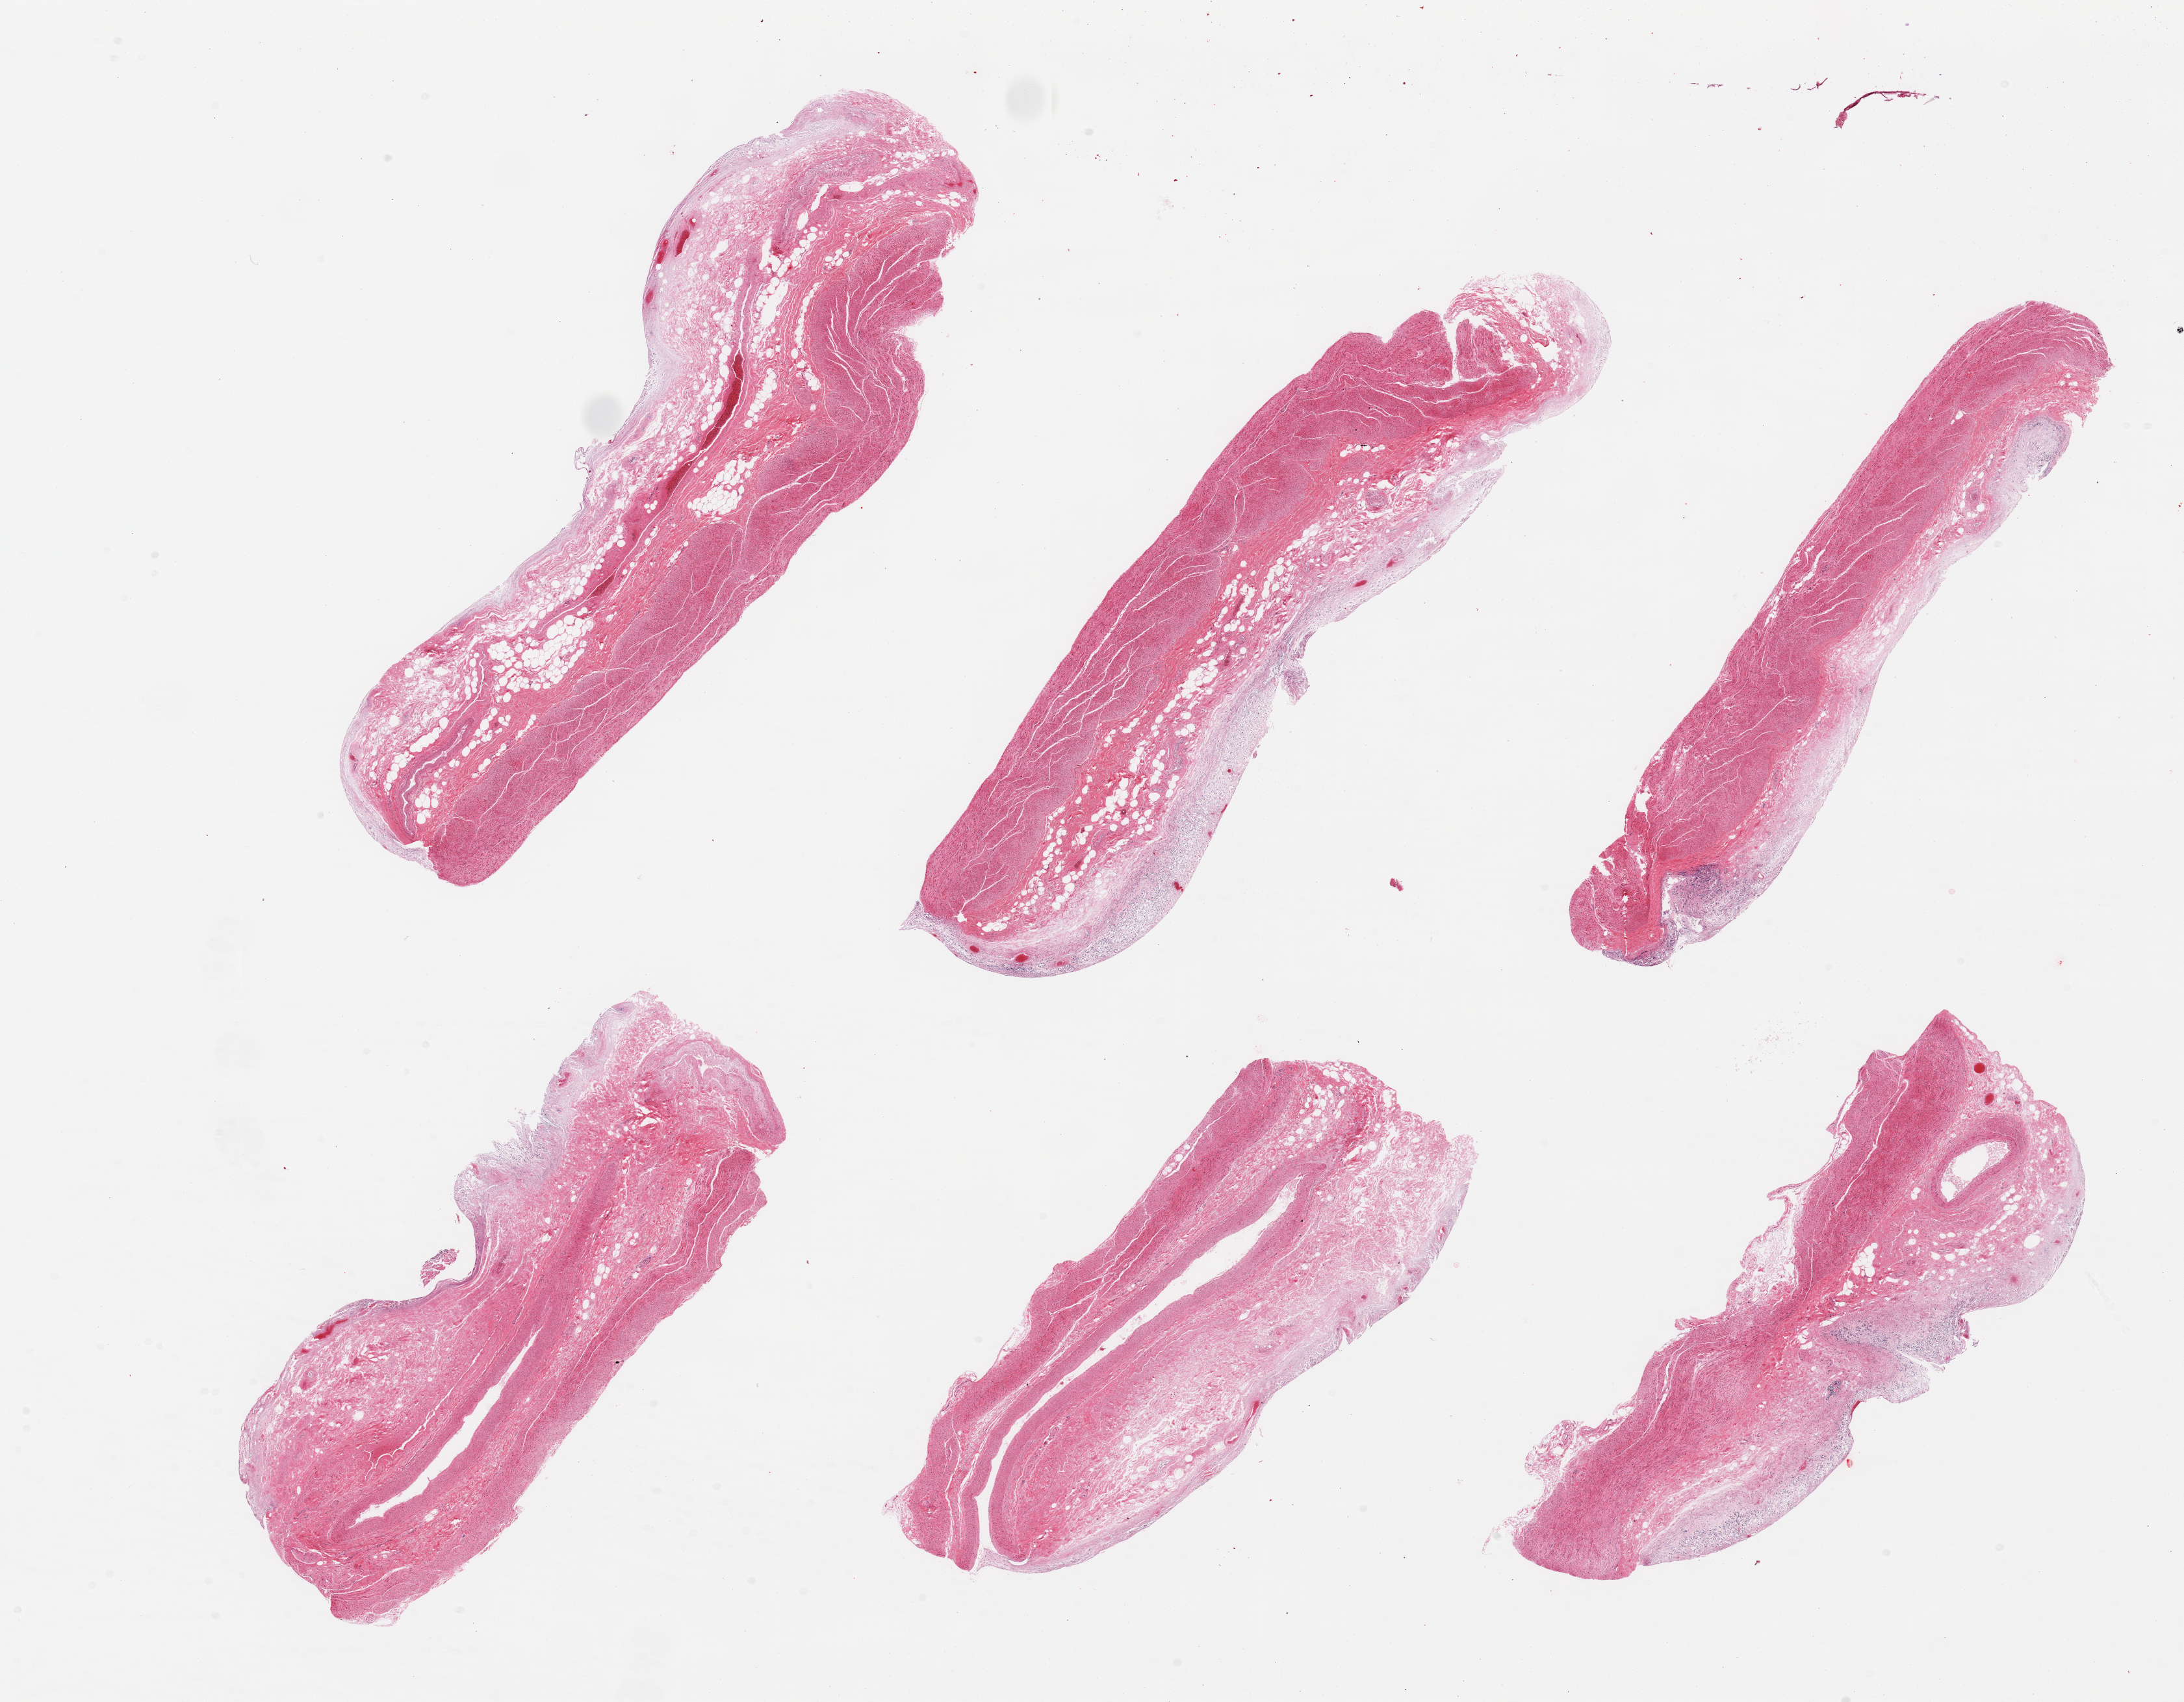
Digitized hematoxylin and eosin (H&E)-stained section, brightfield, low-resolution overview of the scanned area, about 26.6 x 20.7 mm. PAXgene-fixed paraffin-embedded (PFPE) section. Target tissue: stomach. Tissue donor sample. Male donor.
• reviewer comment on this tissue sample: 6 pieces, target mucosa up to ~0.5mm, advanced autolysis